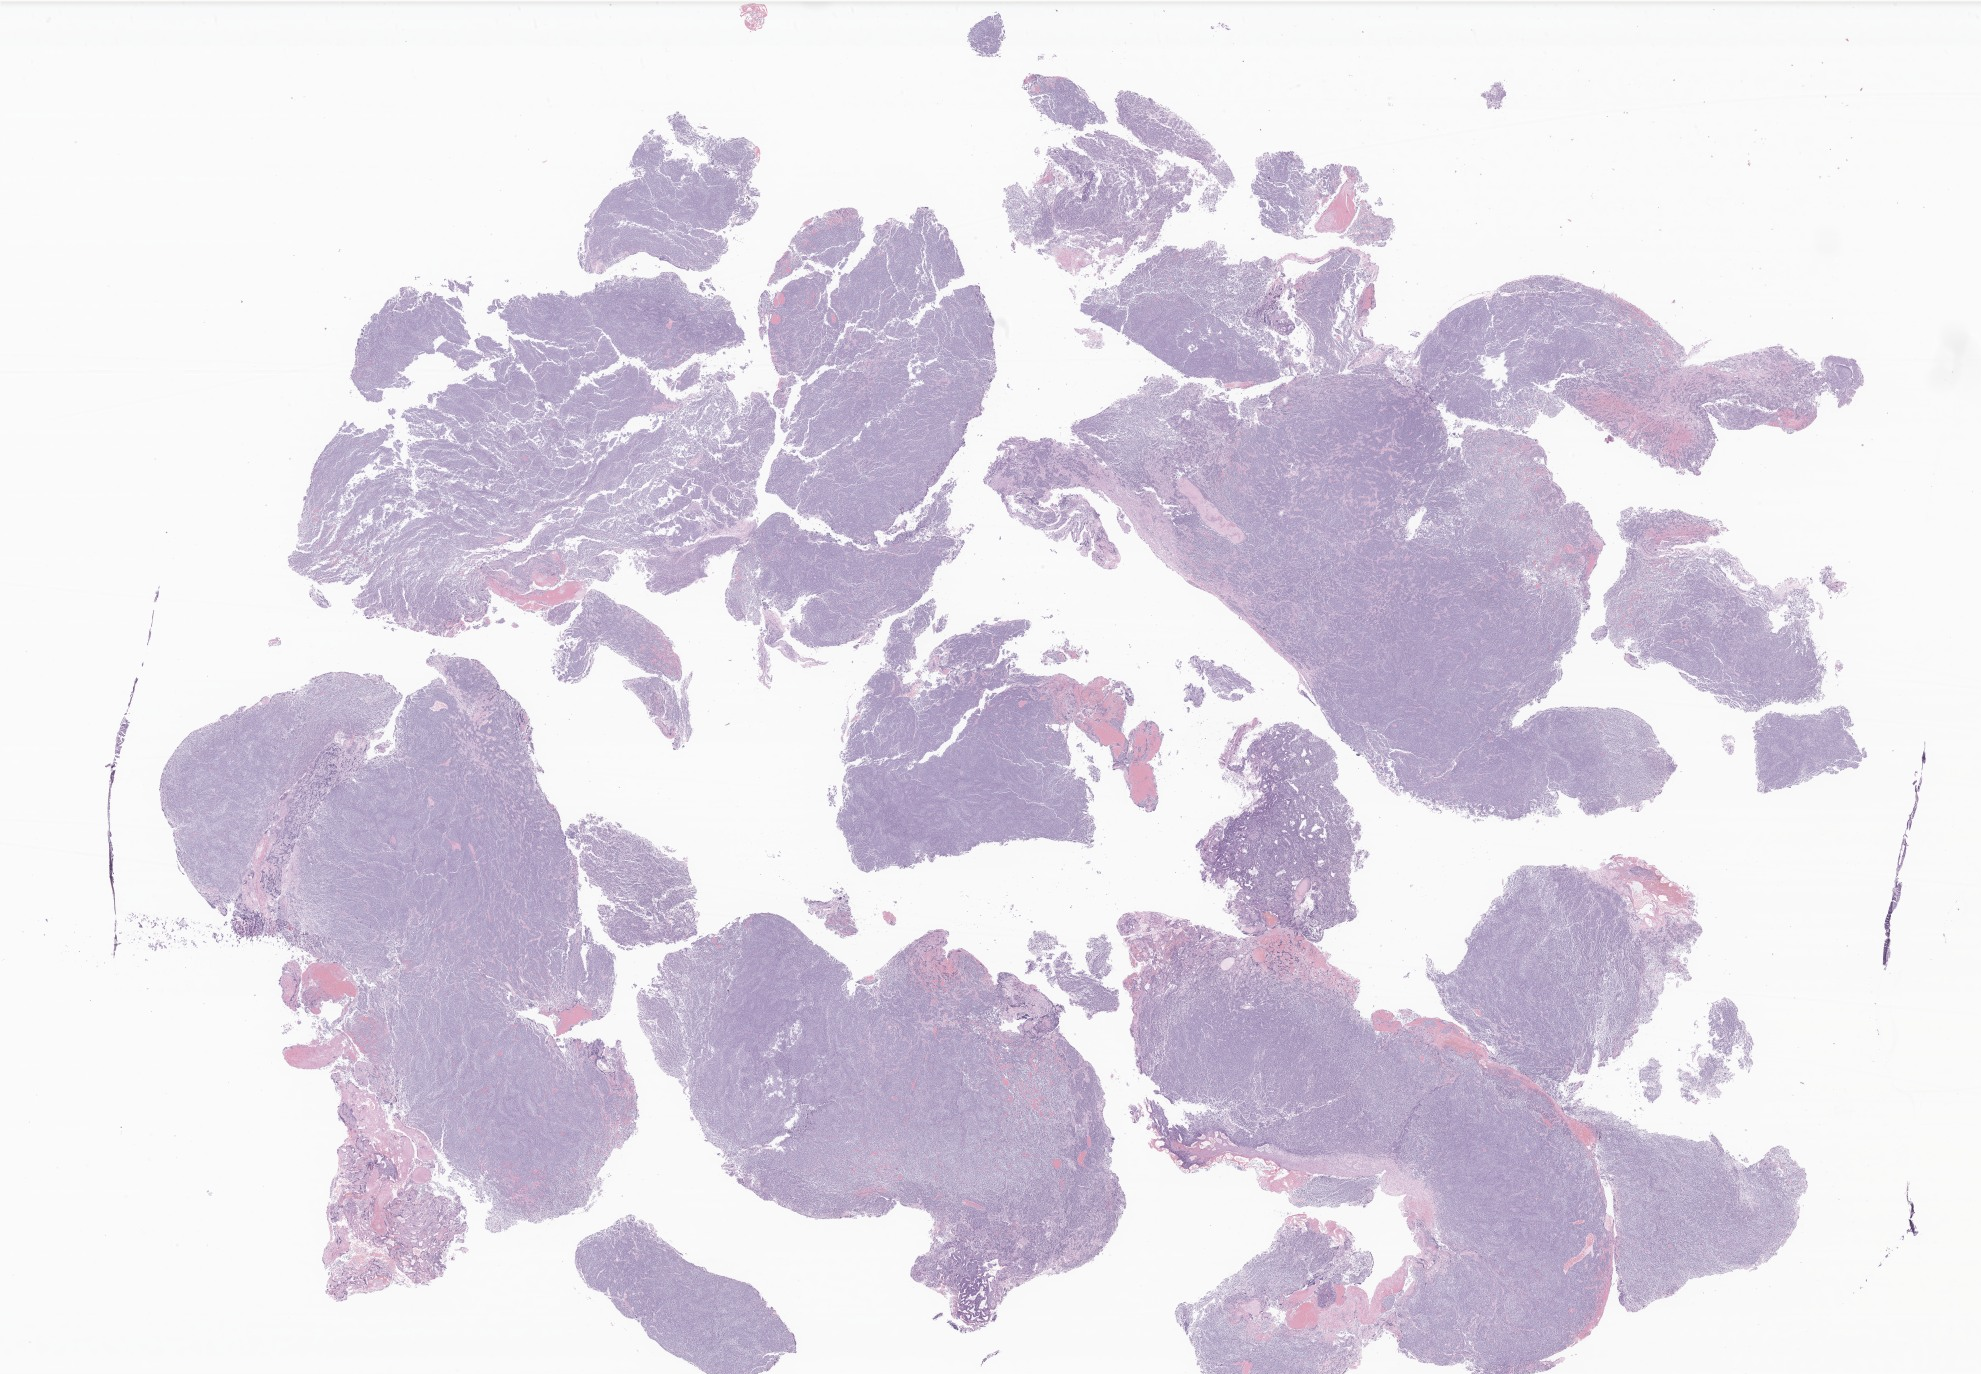
Whole-slide image, hematoxylin and eosin (H&E) stain of tumor tissue from the cerebellum, shown as a low-resolution overview of the whole scanned area (about 33.4 x 23.2 mm), FFPE section. Male patient, age 159 months (13 years 3 months).
- recorded diagnosis: Desmoplastic nodular medulloblastoma